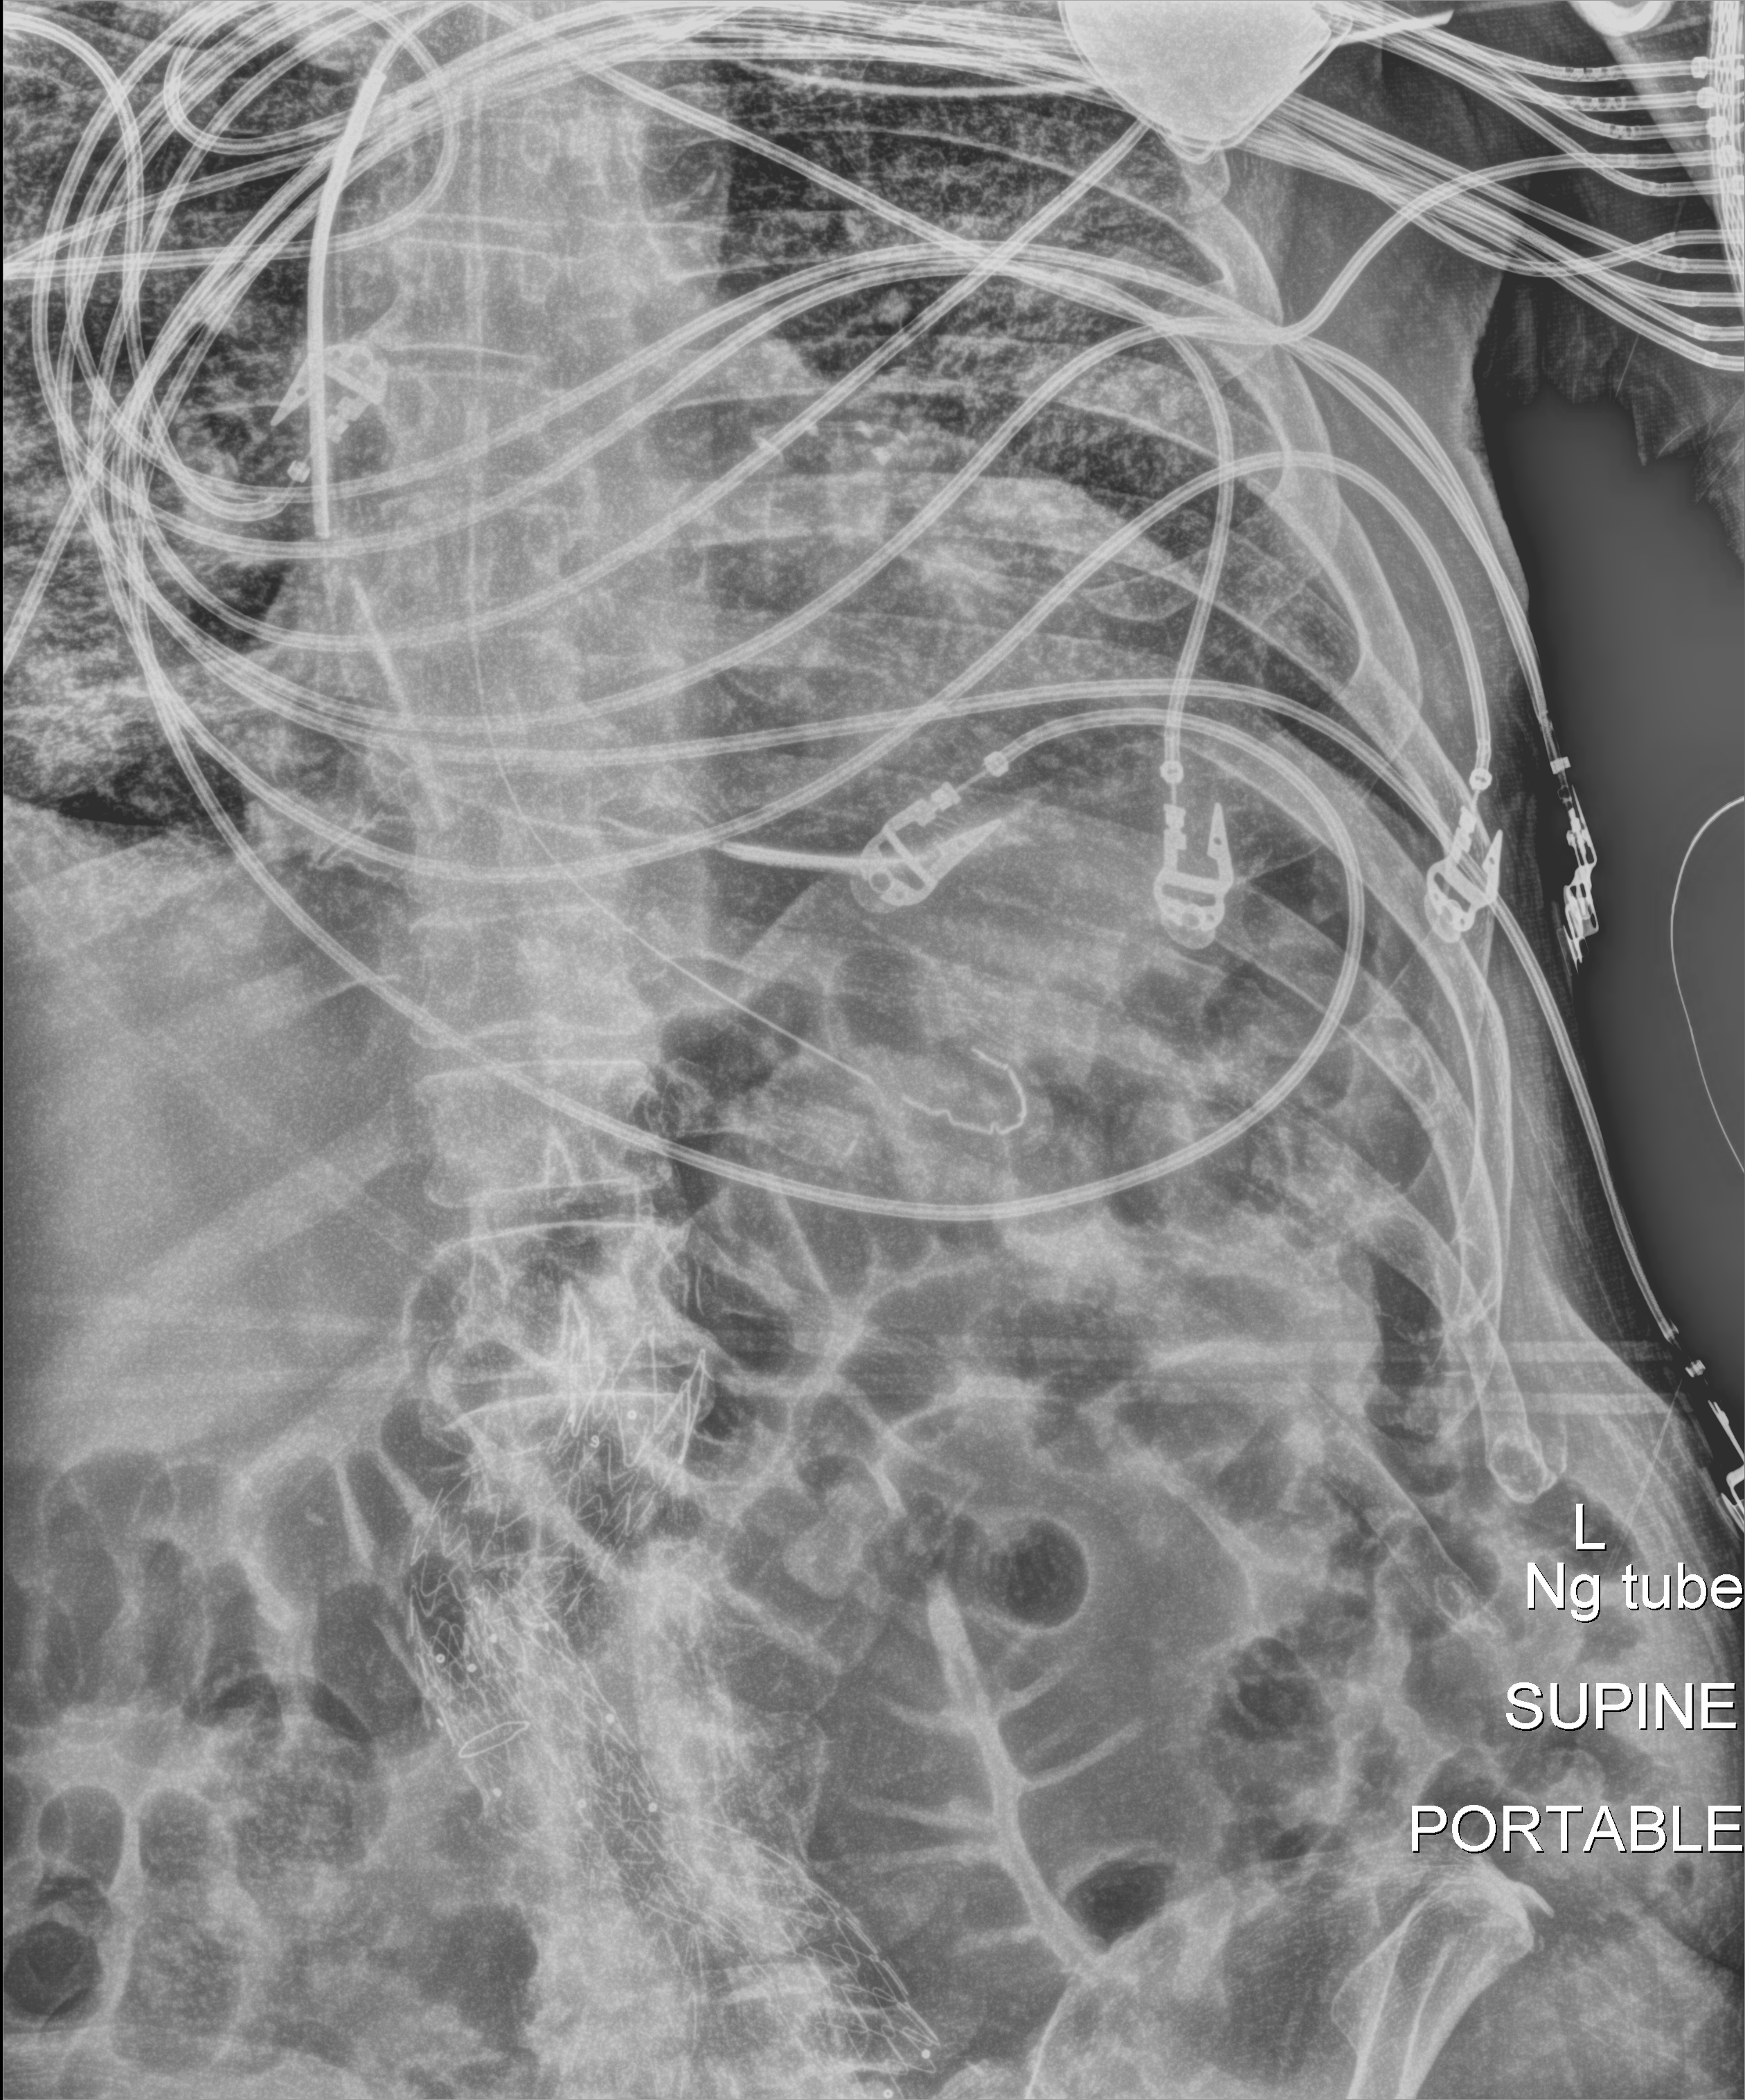
Abdomen X-ray (portable). Male patient hospitalised with COVID-19, age 60–74 years.
Hospital-stay facts (about this admission, not read from this image; timing relative to this image not recorded): admitted to intensive care during this hospital stay: yes; length of hospital stay: 36 days; diabetes (admission record): yes.